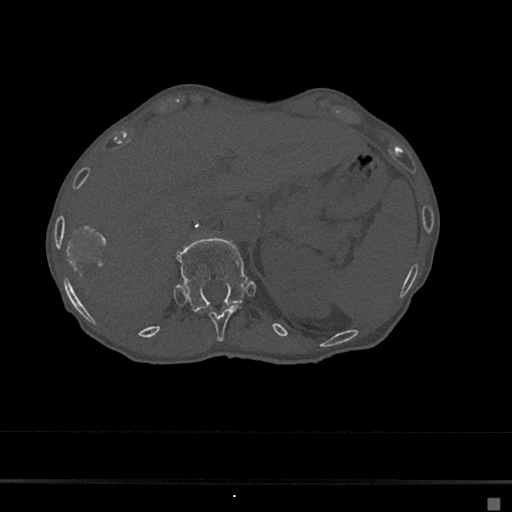
CT including the spine, one axial slice. Slice 138 of 797 in the series (ordered by position). 120 kVp. Bone window (W 1800 / L 400 HU). 0.5 mm slice thickness. 512 × 512 image matrix, field of view 360 × 360 mm. Female patient, age 68 years. From the clinical record (not read from this slice): primary cancer: renal.
Outlined on this slice (semi-automatic segmentation, software-assisted and operator-edited):
- T11 vertebra: bounding box [x1, y1, x2, y2] px = [200, 307, 240, 341]
- T12 vertebra: [176, 237, 248, 311]